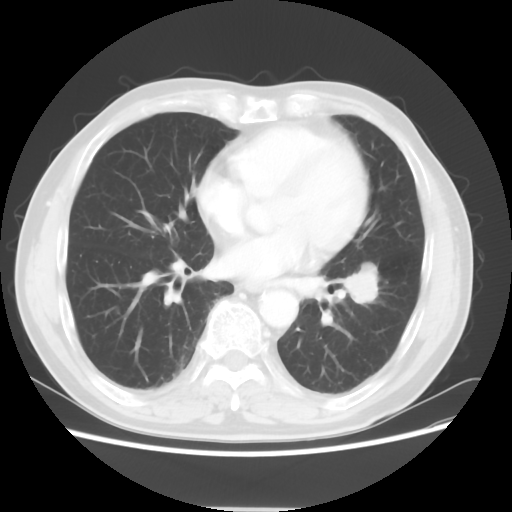
Chest CT, one axial slice; slice 24 of 64 in the series (ordered by position); reconstruction kernel STANDARD; lung window (W 1500 / L -600 HU); 5 mm slice thickness; 512 × 512 image matrix, field of view 366 × 366 mm. Patient: male, 71 years. From the clinical record (not read from this slice): clinical TNM (as recorded): T1c N1 M0.
Outlined on this slice (rectangle marked by the reading radiologist):
- lung tumour (recorded histology: adenocarcinoma): bounding box [x1, y1, x2, y2] px = [342, 260, 386, 312]